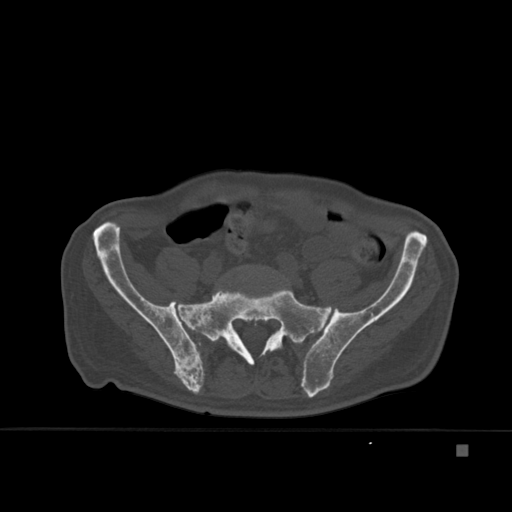
CT including the spine, one axial slice. Bone window (W 1800 / L 400 HU). 1.5 mm slice thickness. 512 × 512 image matrix, field of view 378 × 378 mm. Male patient, age 75 years. Case-level facts recorded for this patient, not image findings: primary cancer: prostate.
Outlined on this slice (semi-automatic segmentation, software-assisted and operator-edited):
- L5 vertebra: bounding box [x1, y1, x2, y2] px = [242, 342, 244, 345]